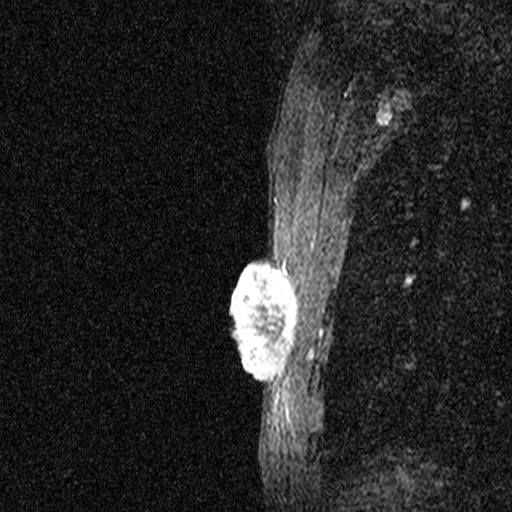
Breast MRI (dynamic contrast-enhanced), one sagittal slice; slice 36 of 44 in the series (ordered by position); dynamic contrast-enhanced study with each time point stored as its own series, time point 2 of 3 at this slice position (early post-contrast, ordered by acquisition time); 1.5 T; TE 4.5 ms, TR 11 ms; 512 × 512 image matrix, field of view 200 × 200 mm. Patient: female, 44 years. Case-level facts recorded for this patient, not image findings: setting: breast cancer imaged before/during neoadjuvant chemotherapy; receptor status: HR-positive, HER2-negative.
Annotated regions visible in this slice (semi-automatically segmented with operator editing):
- analysis volume of interest (the breast-tissue region the enhancement analysis was run in; not a lesion): box from (x=204, y=254) to (x=309, y=401) px
- tumour enhancement mask (voxels above the 90 % enhancement threshold inside the analysis volume of interest): (x=230, y=256)–(x=301, y=401)